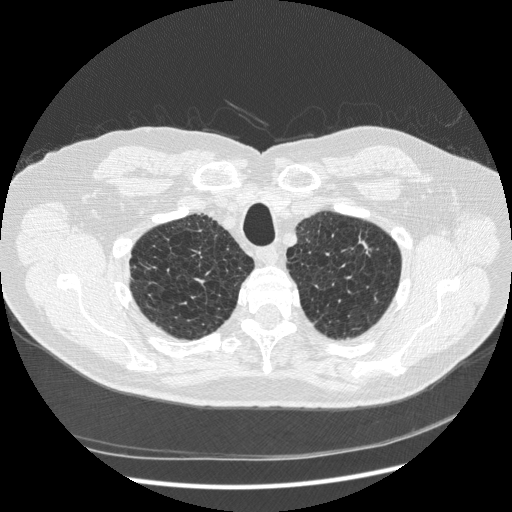
Axial slice from a low-dose chest CT screening exam; first (baseline) screen; lung window (W 1500 / L -600 HU); 1.25 mm slice thickness; slice 39 of 265 in the series; 512 × 512 image matrix, field of view 380 × 380 mm. Male, age 70 years at enrolment. Former smoker at enrolment.
• Expert-annotated lung lesion, box from (x=332, y=219) to (x=387, y=274) px.
• The screening reader recorded 2 non-calcified nodules or masses ≥4 mm on this exam (right lower lobe, right lower lobe); which of them this box marks is not recorded.
• Lung cancer was diagnosed 816 days after this screen (after the third annual screen): squamous cell carcinoma, NOS, left upper lobe, moderately differentiated (G2), stage IA (AJCC 6th edition), 18 mm at pathology.